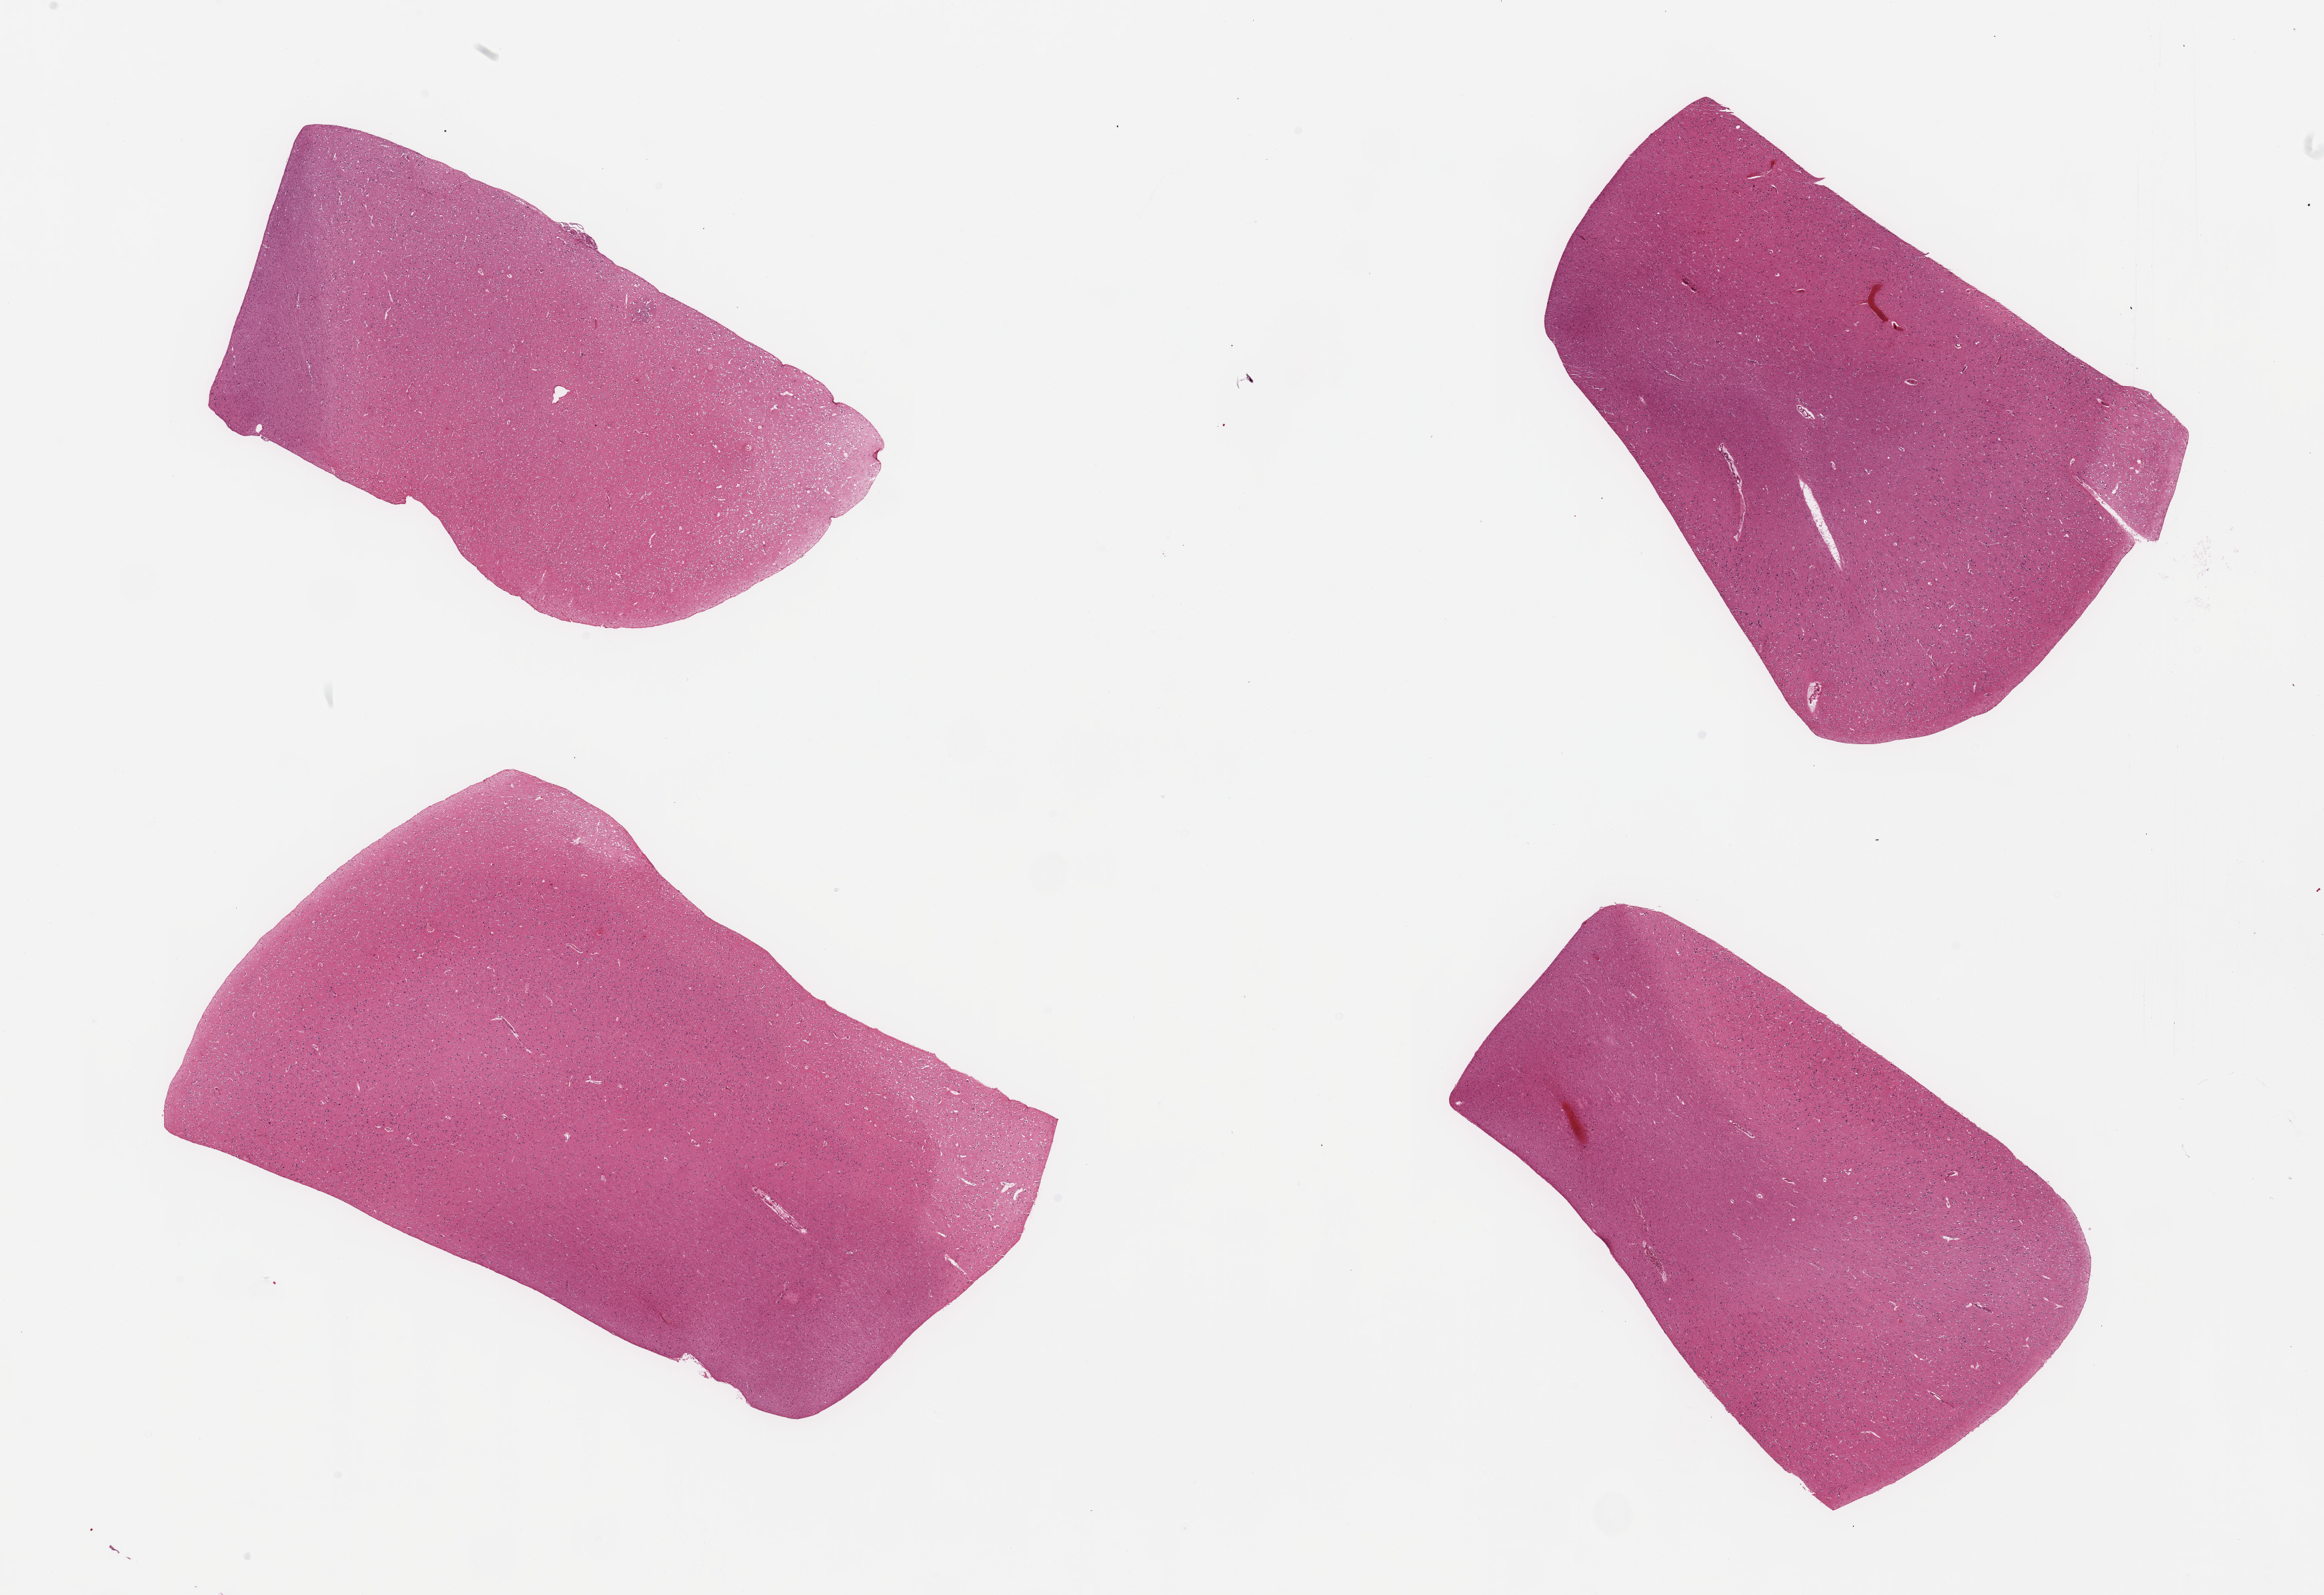
H&E whole-slide image — shown as a low-resolution overview of the whole scanned area (about 27.6 x 18.9 mm, acquisition: 20x scan), PAXgene-fixed paraffin-embedded (PFPE) section, sampled site (target tissue): cerebral cortex, tissue donor sample. Male donor.
- review note (as recorded): 4 pieces